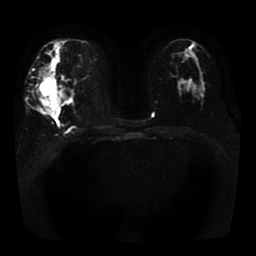
Breast MRI, one axial slice; position 21 of 41 along the scan axis; diffusion-weighted series; image 2 of 4 stored at this slice position (different b-values; order by instance number); 1.5 T; 5 mm slice thickness; 256 × 256 image matrix, field of view 330 × 330 mm. Female patient.
Outlined on this slice (expert manual segmentation):
- tumour on diffusion-weighted imaging: bounding box (x1, y1, x2, y2) in pixels: (39, 75, 59, 114)